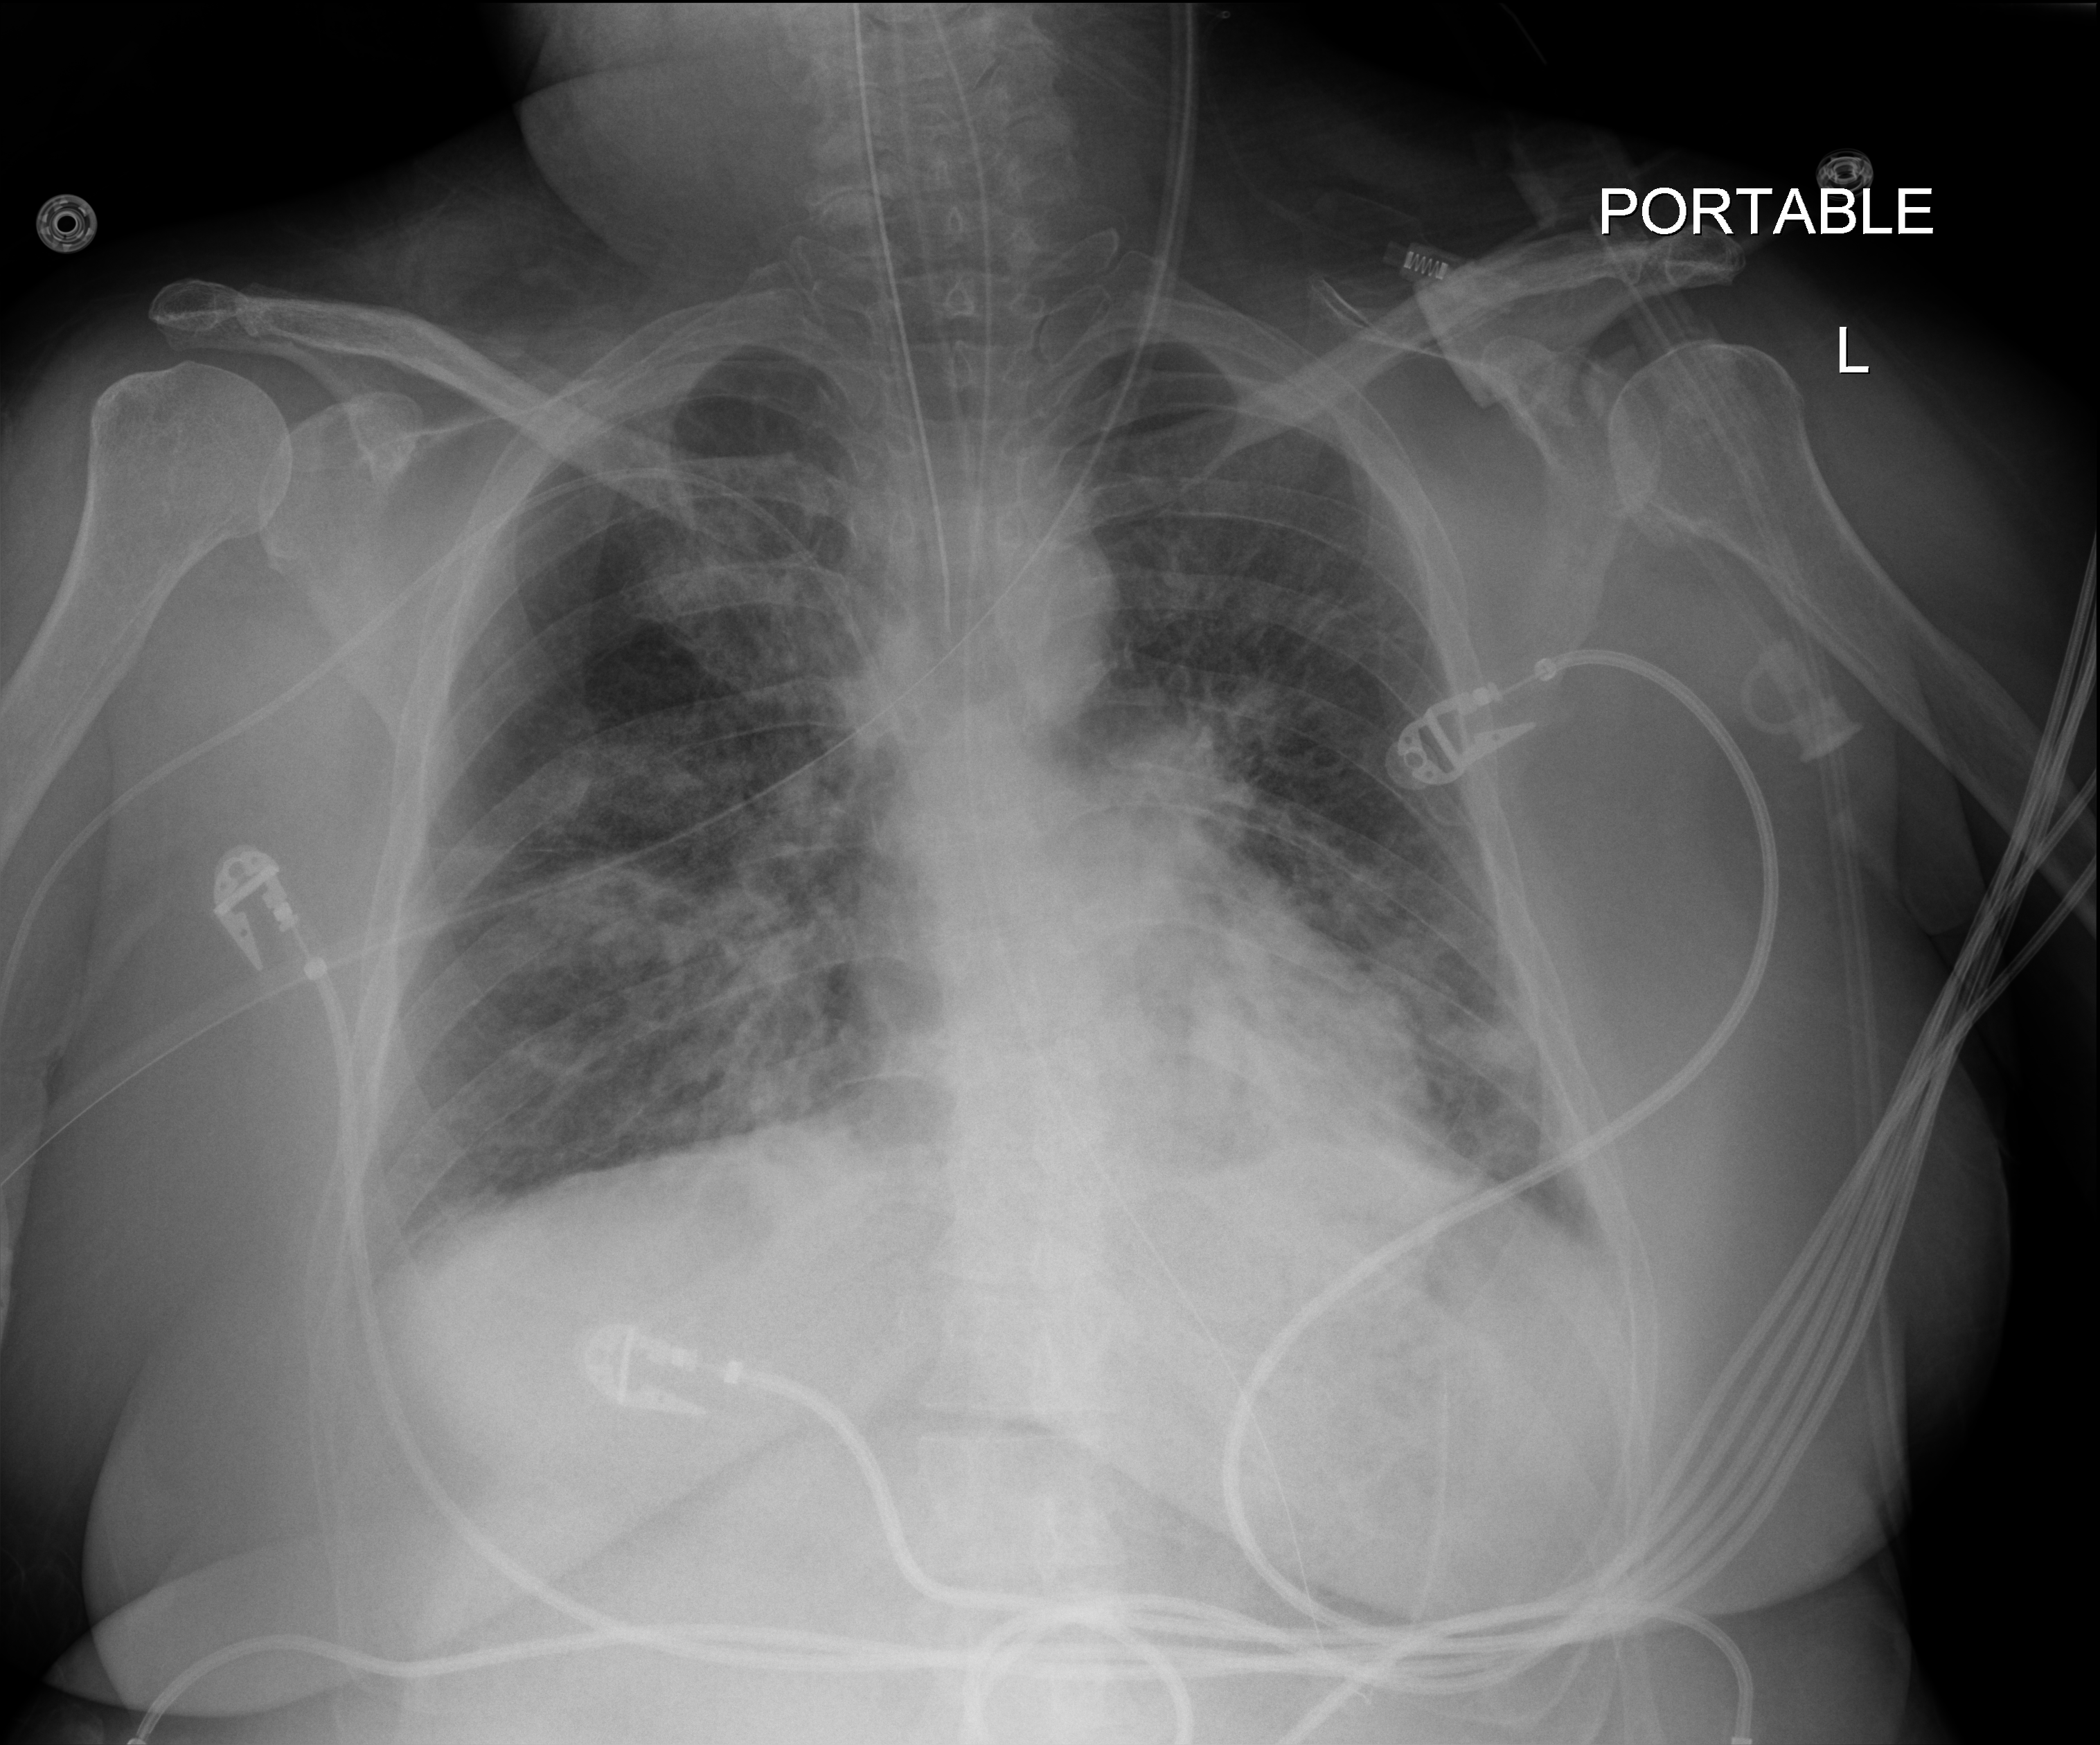
Chest radiograph (digital radiography), anteroposterior (AP) projection. Patient hospitalised with COVID-19, aged 18–59 years.
From the hospital-stay record, not from the radiograph (when in the stay this image was taken is not recorded):
- admitted to intensive care during this hospital stay: yes
- length of hospital stay: 15 days